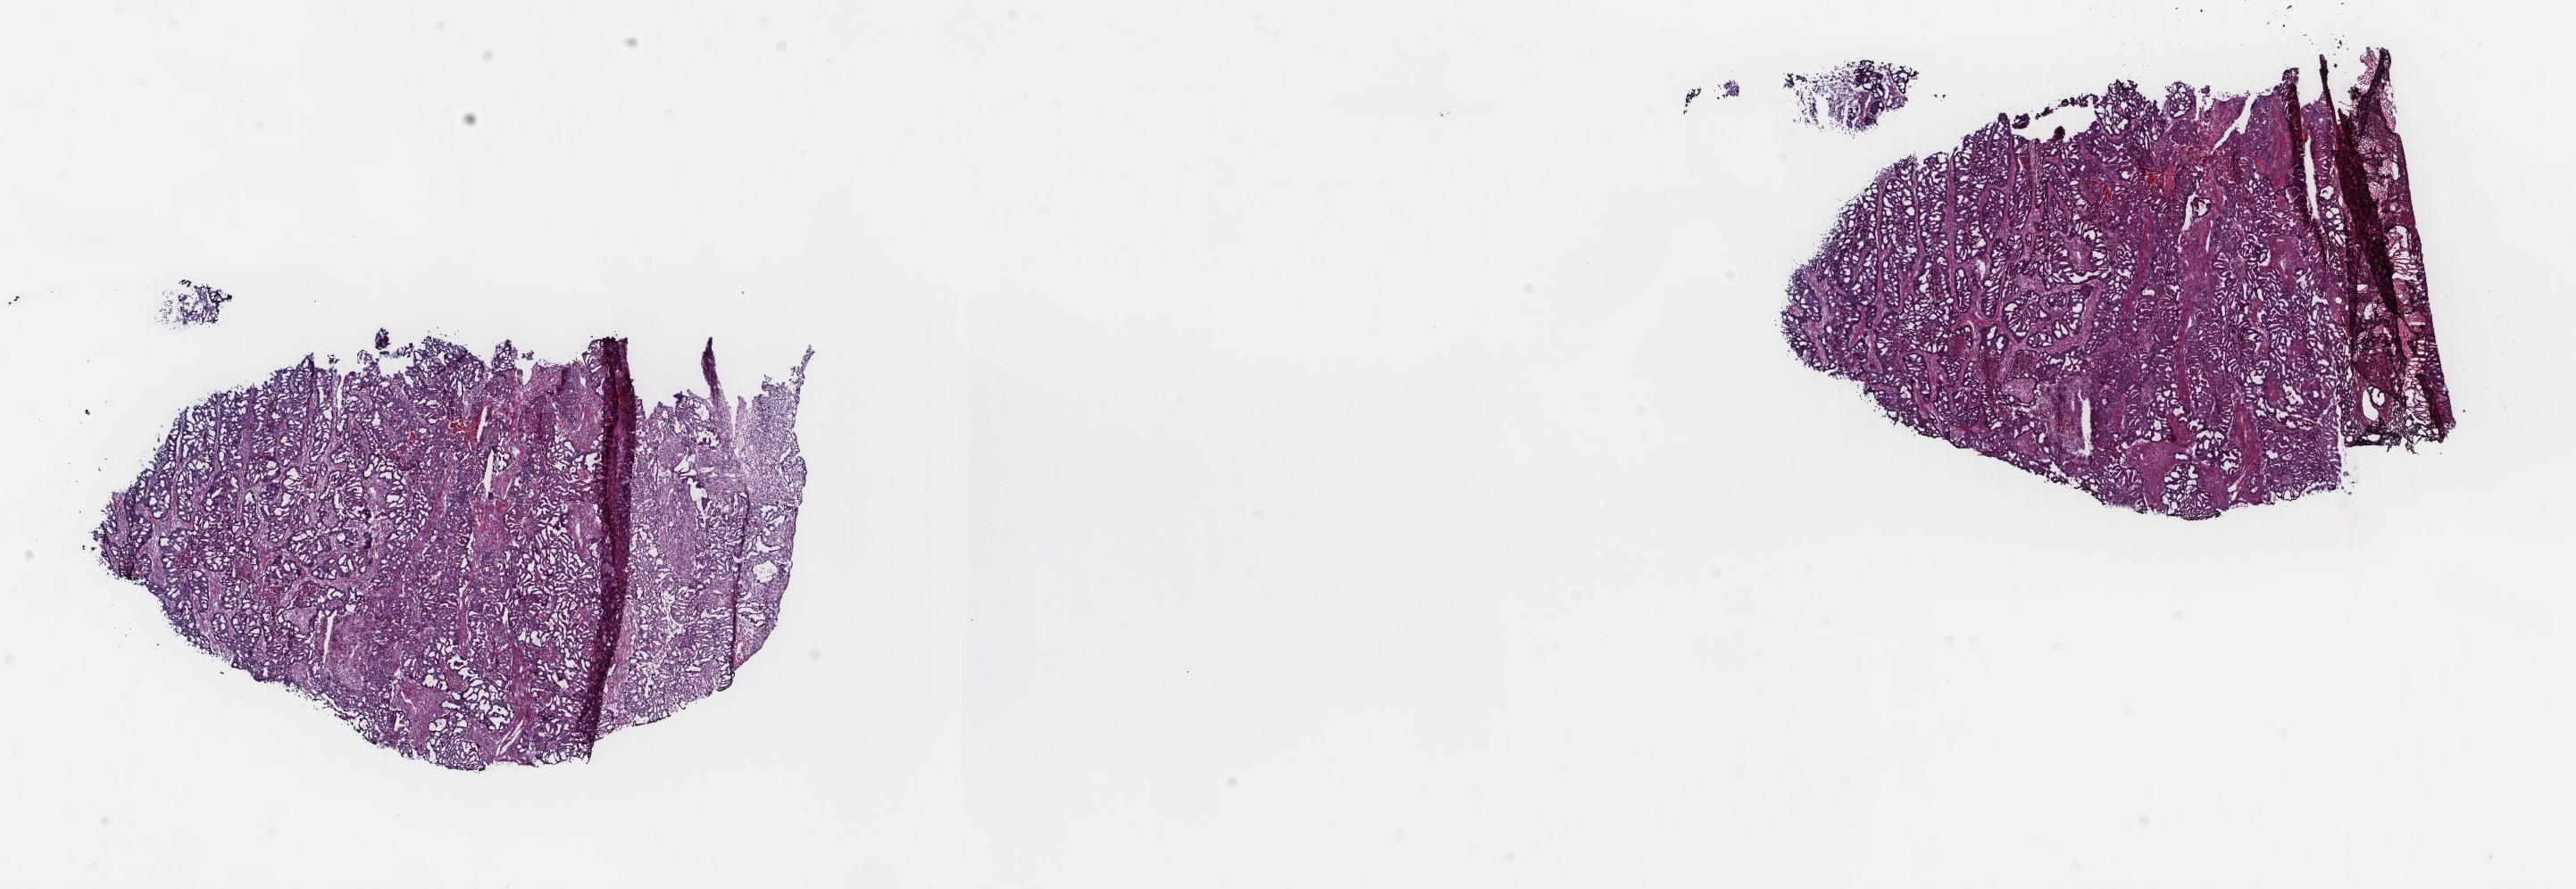
H&E-stained whole-slide image, shown as a low-resolution overview of the whole scanned area (about 22.9 x 7.9 mm, slide scanned at 40x). Frozen section. Sample: primary tumour, uterus. Patient: female, age at initial diagnosis 51 years. Histologic grade: G2 (moderately differentiated). Slide review estimates, as recorded: tumour cells 70%, tumour nuclei 70%, normal cells 0%, stromal cells 25%, necrosis 5%. Inflammatory infiltration, as recorded: lymphocyte infiltration 40%, monocyte infiltration 20%, neutrophil infiltration 20%.
Lymph nodes positive (case pathology): 0 of 6 examined. FIGO stage: II. Pathologic diagnosis: Endometrioid adenocarcinoma, NOS.